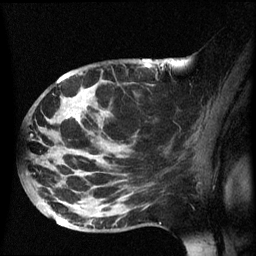
Breast MRI (dynamic contrast-enhanced), one sagittal slice. Position 37 of 60 along the scan axis. Dynamic contrast-enhanced series, image 2 of 3 at this slice position (ordered by acquisition). 1.5 T. TE 4.2 ms, TR 8.4 ms. 2.5 mm slice thickness. 256 × 256 image matrix, field of view 220 × 220 mm. Female patient, age 49 years.
Annotated regions visible in this slice (semi-automatically segmented with operator editing):
- analysis volume of interest (the breast-tissue region the enhancement analysis was run in; not a lesion): bounding box <26,72,162,233> (left, top, right, bottom; pixels)
- tumour enhancement mask (voxels above the 70 % enhancement threshold inside the analysis volume of interest): <68,114,81,123>